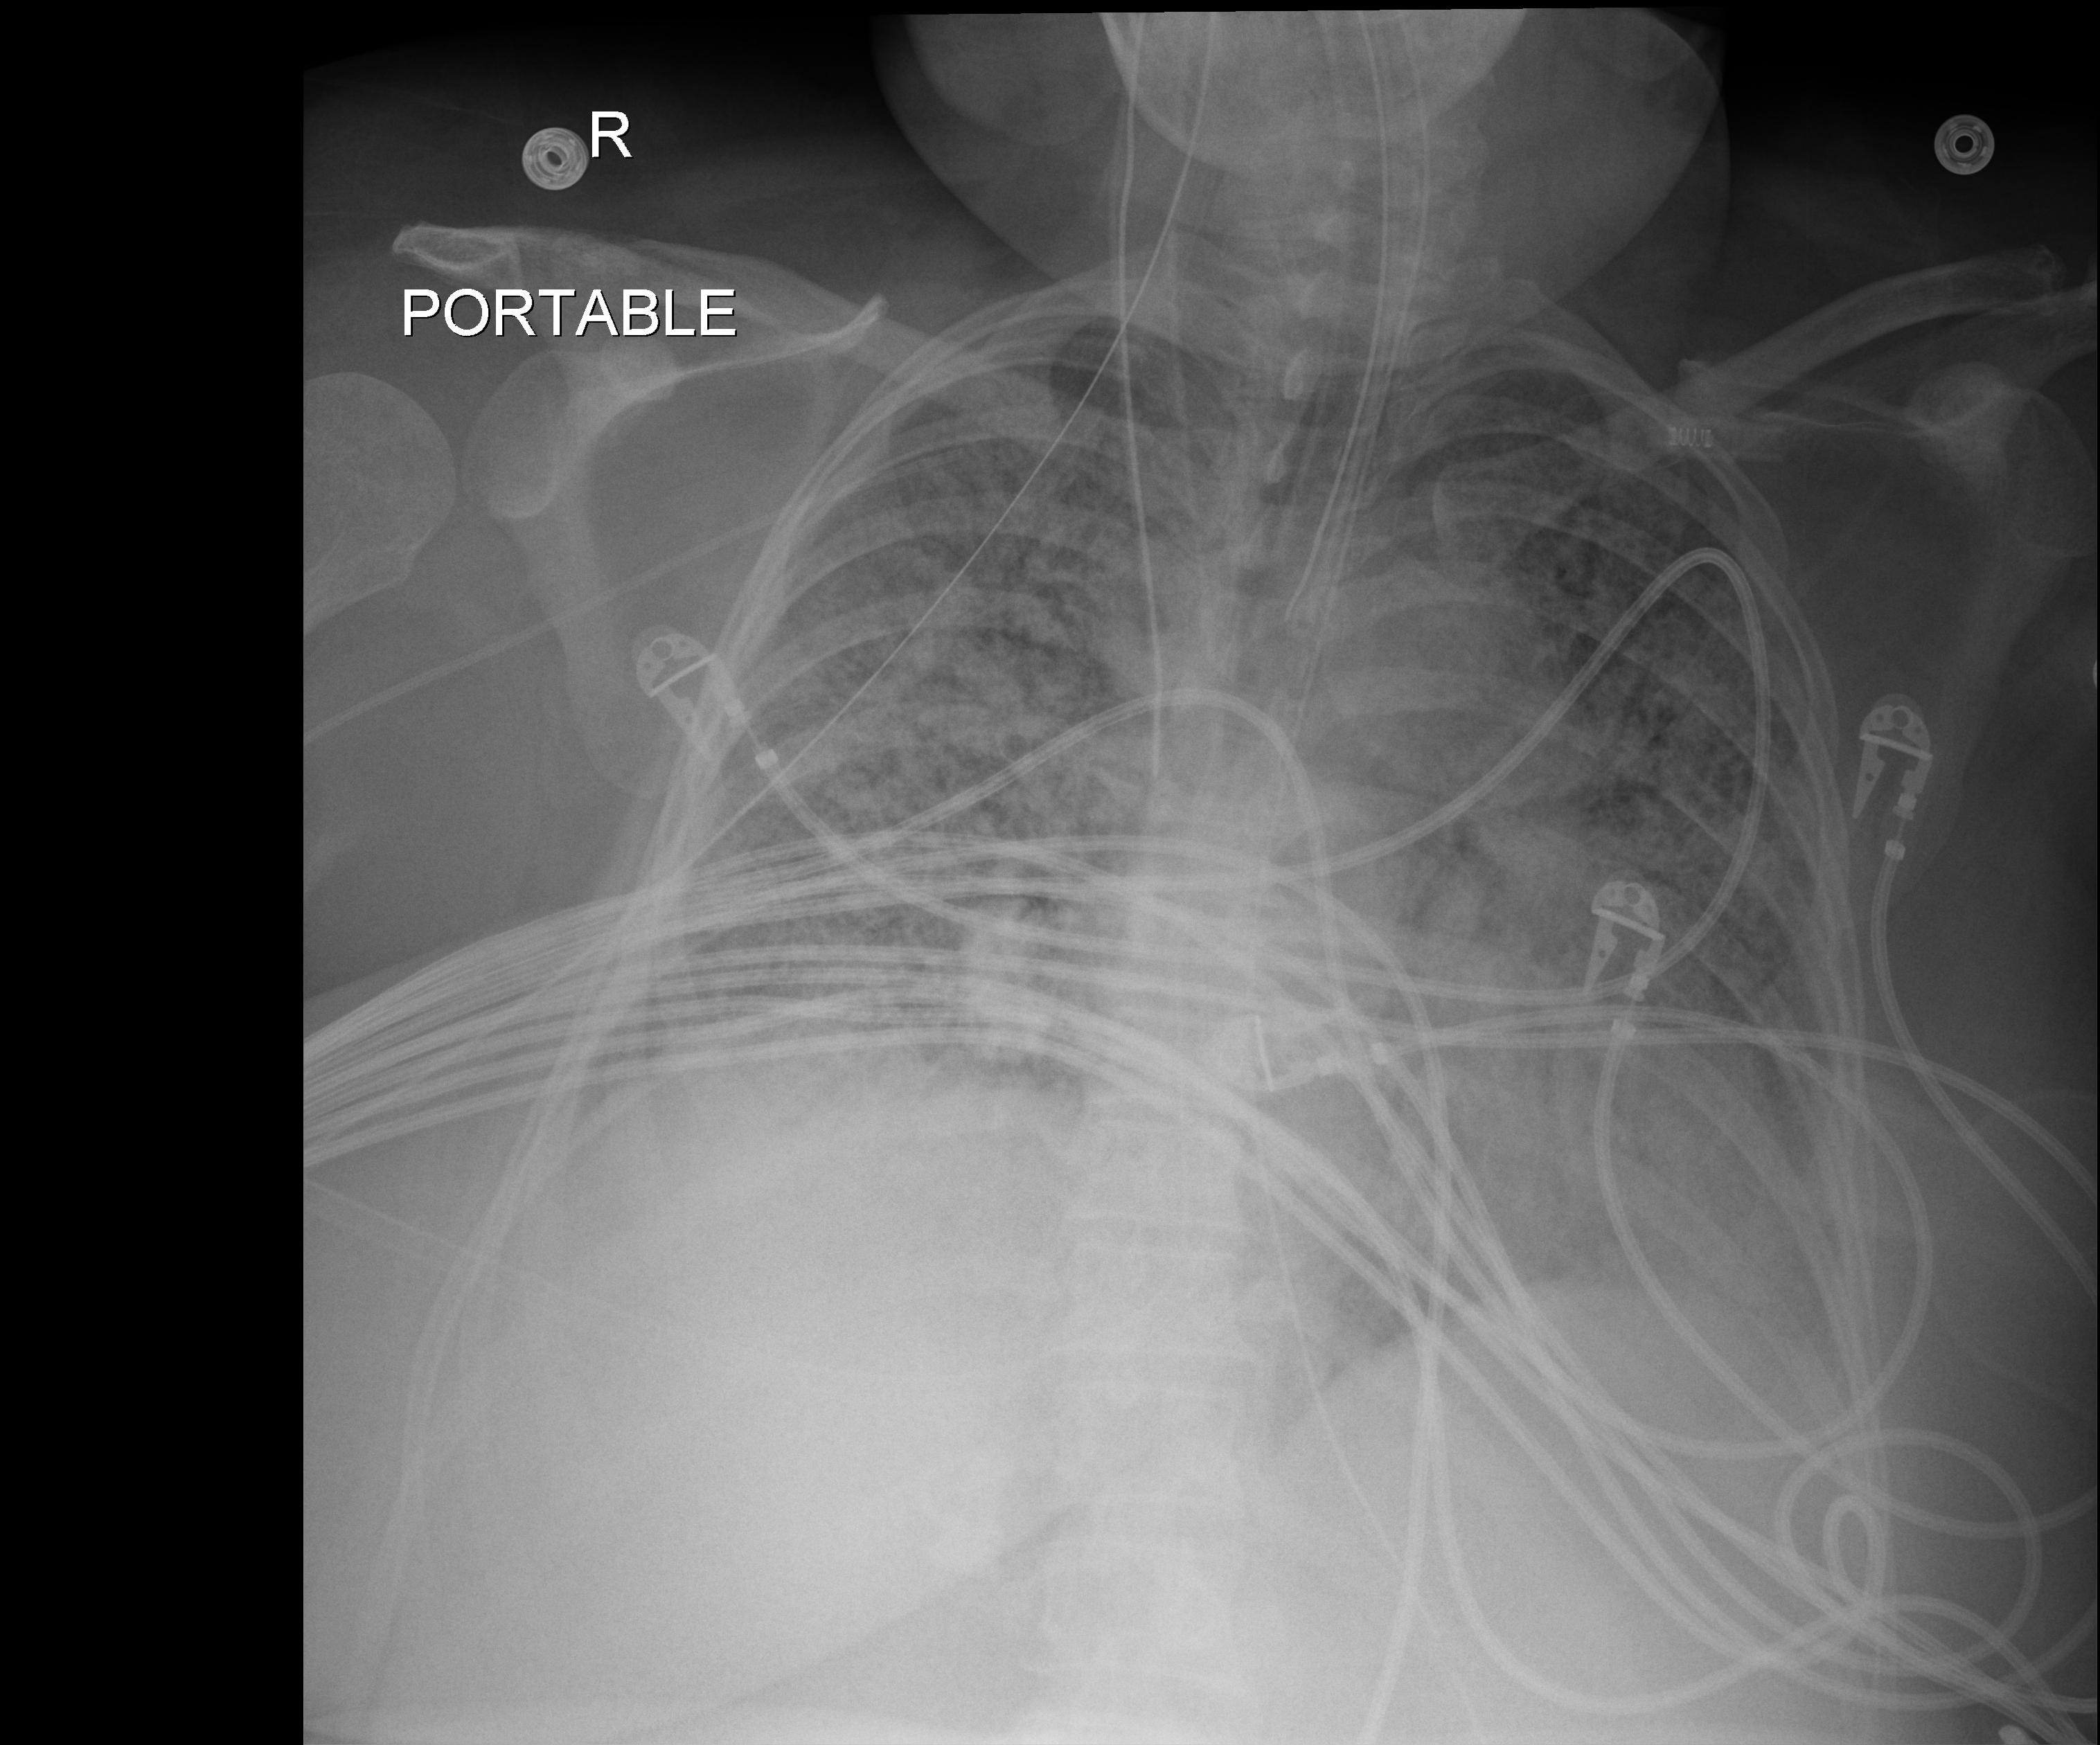
Bedside chest radiograph (digital radiography); anteroposterior (AP) projection. Patient hospitalised with COVID-19; female, aged 18–59 years.
Admission-level facts for this patient (not findings on this image; timing relative to this image not recorded):
- mechanically ventilated during this hospital stay: yes